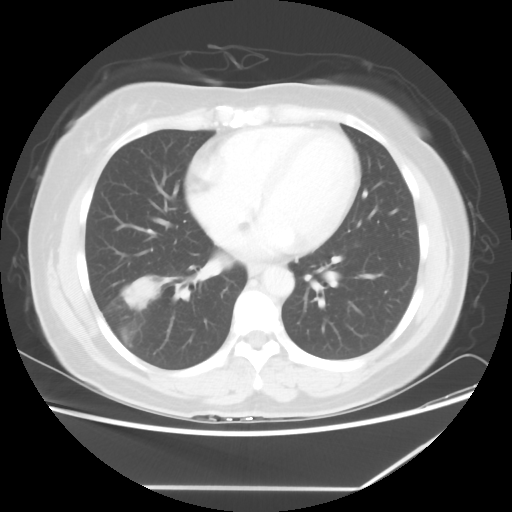
Chest CT, one axial slice. Slice 26 of 60 in the series (ordered by position). Reconstruction kernel STANDARD. 100 kVp. Lung window (W 1500 / L -600 HU). 5 mm slice thickness. 512 × 512 image matrix, field of view 374 × 374 mm. Patient: female, 42 years. Case-level facts recorded for this patient, not image findings: clinical TNM (as recorded): T2 N1 M0.
Outlined on this slice (rectangle marked by the reading radiologist):
- lung tumour (recorded histology: adenocarcinoma): bounding box (x1, y1, x2, y2) in pixels: (116, 273, 160, 312)